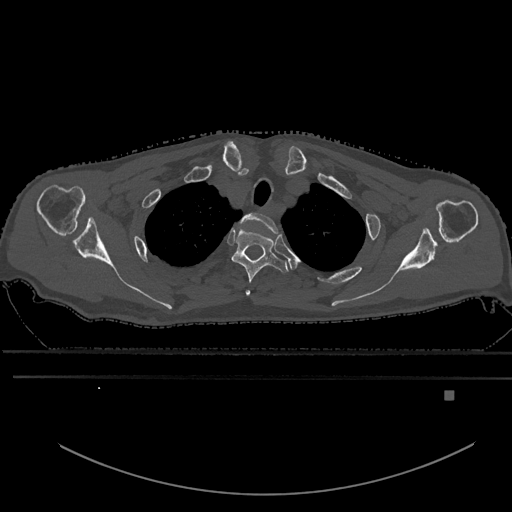
CT including the spine, one axial slice; position 498 of 969 along the scan axis; bone window (W 1800 / L 400 HU); 512 × 512 image matrix, field of view 456 × 456 mm. Male patient, age 82 years. Case-level facts recorded for this patient, not image findings: primary cancer: prostate; vertebrae with lytic lesions (as recorded): T11, T9, T8, T2.
Outlined on this slice (semi-automatically segmented with operator editing):
- T1 vertebra: bounding box <240,212,278,233> (left, top, right, bottom; pixels)
- T2 vertebra: <231,227,288,295>